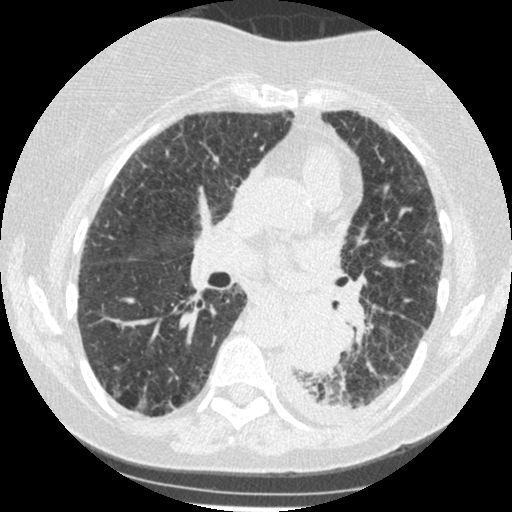
Axial slice from a low-dose chest CT screening exam, third screening round (two years after baseline), lung window (W 1500 / L -600 HU), 1.25 mm slice thickness, standard (soft-tissue) reconstruction kernel (STANDARD), 512 × 512 image matrix, field of view 310 × 310 mm. Female participant, aged 60 years at enrolment. Former smoker at enrolment.
Lesion marked by an expert reader, bounding box <272,306,342,374> (left, top, right, bottom; pixels). Reader record for this screening exam (exam-level; its link to the box is not recorded): non-calcified nodule or mass ≥4 mm, left lower lobe, 54 × 38 mm, smooth margins, soft tissue attenuation, pre-existing on the prior screen: yes; interval growth: yes. Official screen result: positive, other. Later outcome: lung cancer diagnosed 15 days after this screen — small cell carcinoma, NOS, left lower lobe, undifferentiated (G4), stage IV (AJCC 6th edition), 69 mm at pathology.